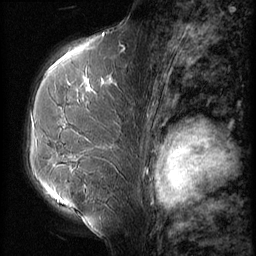
Breast MRI (dynamic contrast-enhanced), one sagittal slice; position 38 of 56 along the scan axis; 3 images stored at this slice position (order not interpretable as contrast timing); 1.5 T; TE 4.2 ms, TR 9 ms; 2.5 mm slice thickness; 256 × 256 image matrix. Patient: female, 51 years. From the clinical record (not read from this slice): setting: breast cancer imaged before/during neoadjuvant chemotherapy; receptor status: HR-positive, HER2-negative.
Structures marked on this image (semi-automatic segmentation, software-assisted and operator-edited):
- analysis volume of interest (the breast-tissue region the enhancement analysis was run in; not a lesion): bounding box (x1, y1, x2, y2) in pixels: (23, 56, 142, 165)
- tumour enhancement mask (voxels above the 140 % enhancement threshold inside the analysis volume of interest): (46, 72, 113, 93)